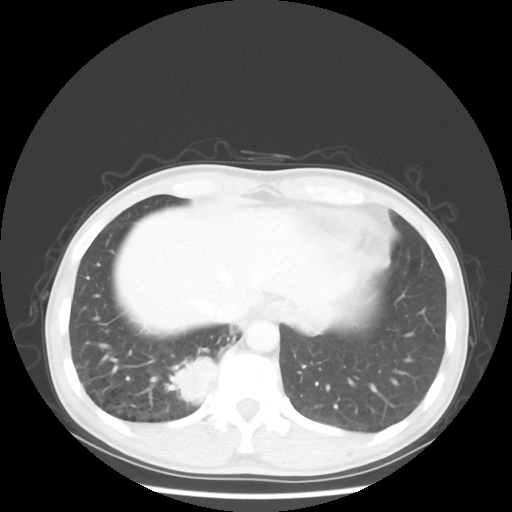
Chest CT, one axial slice. Position 9 of 58 along the scan axis. Reconstruction kernel STANDARD. Lung window (W 1500 / L -600 HU). 512 × 512 image matrix, field of view 360 × 360 mm. Male patient, age 56 years. From the clinical record (not read from this slice): clinical TNM (as recorded): T2 N1 M1; histopathological grade: G1.
Structures marked on this image (rectangle marked by the reading radiologist):
- lung tumour (recorded histology: adenocarcinoma): bounding box [x1, y1, x2, y2] px = [167, 352, 217, 409]